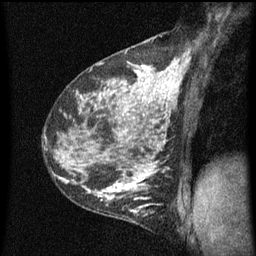
Breast MRI (dynamic contrast-enhanced), one sagittal slice. Slice 36 of 60 in the series (ordered by position). Dynamic contrast-enhanced series, image 2 of 5 at this slice position (ordered by acquisition). 1.5 T. TE 4.2 ms, TR 8 ms. 2 mm slice thickness. 256 × 256 image matrix, field of view 180 × 180 mm. Patient: female, 35 years.
Structures marked on this image (semi-automatic segmentation, software-assisted and operator-edited):
- analysis volume of interest (the breast-tissue region the enhancement analysis was run in; not a lesion): box from (x=118, y=190) to (x=160, y=229) px
- tumour enhancement mask (voxels above the 70 % enhancement threshold inside the analysis volume of interest): (x=126, y=190)–(x=159, y=213)